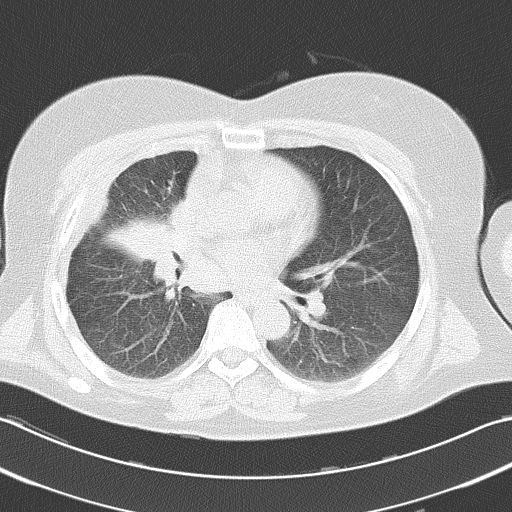
Chest CT, one axial slice; position 17 of 38 along the scan axis; 120 kVp; lung window (W 1500 / L -600 HU); 5 mm slice thickness; 512 × 512 image matrix, field of view 346 × 346 mm. Female patient, age 52 years. Case-level facts recorded for this patient, not image findings: clinical TNM (as recorded): T3 N1 M0.
Annotated regions visible in this slice (rectangle marked by the reading radiologist):
- lung tumour (recorded histology: squamous cell carcinoma): bounding box (x1, y1, x2, y2) in pixels: (105, 209, 178, 299)